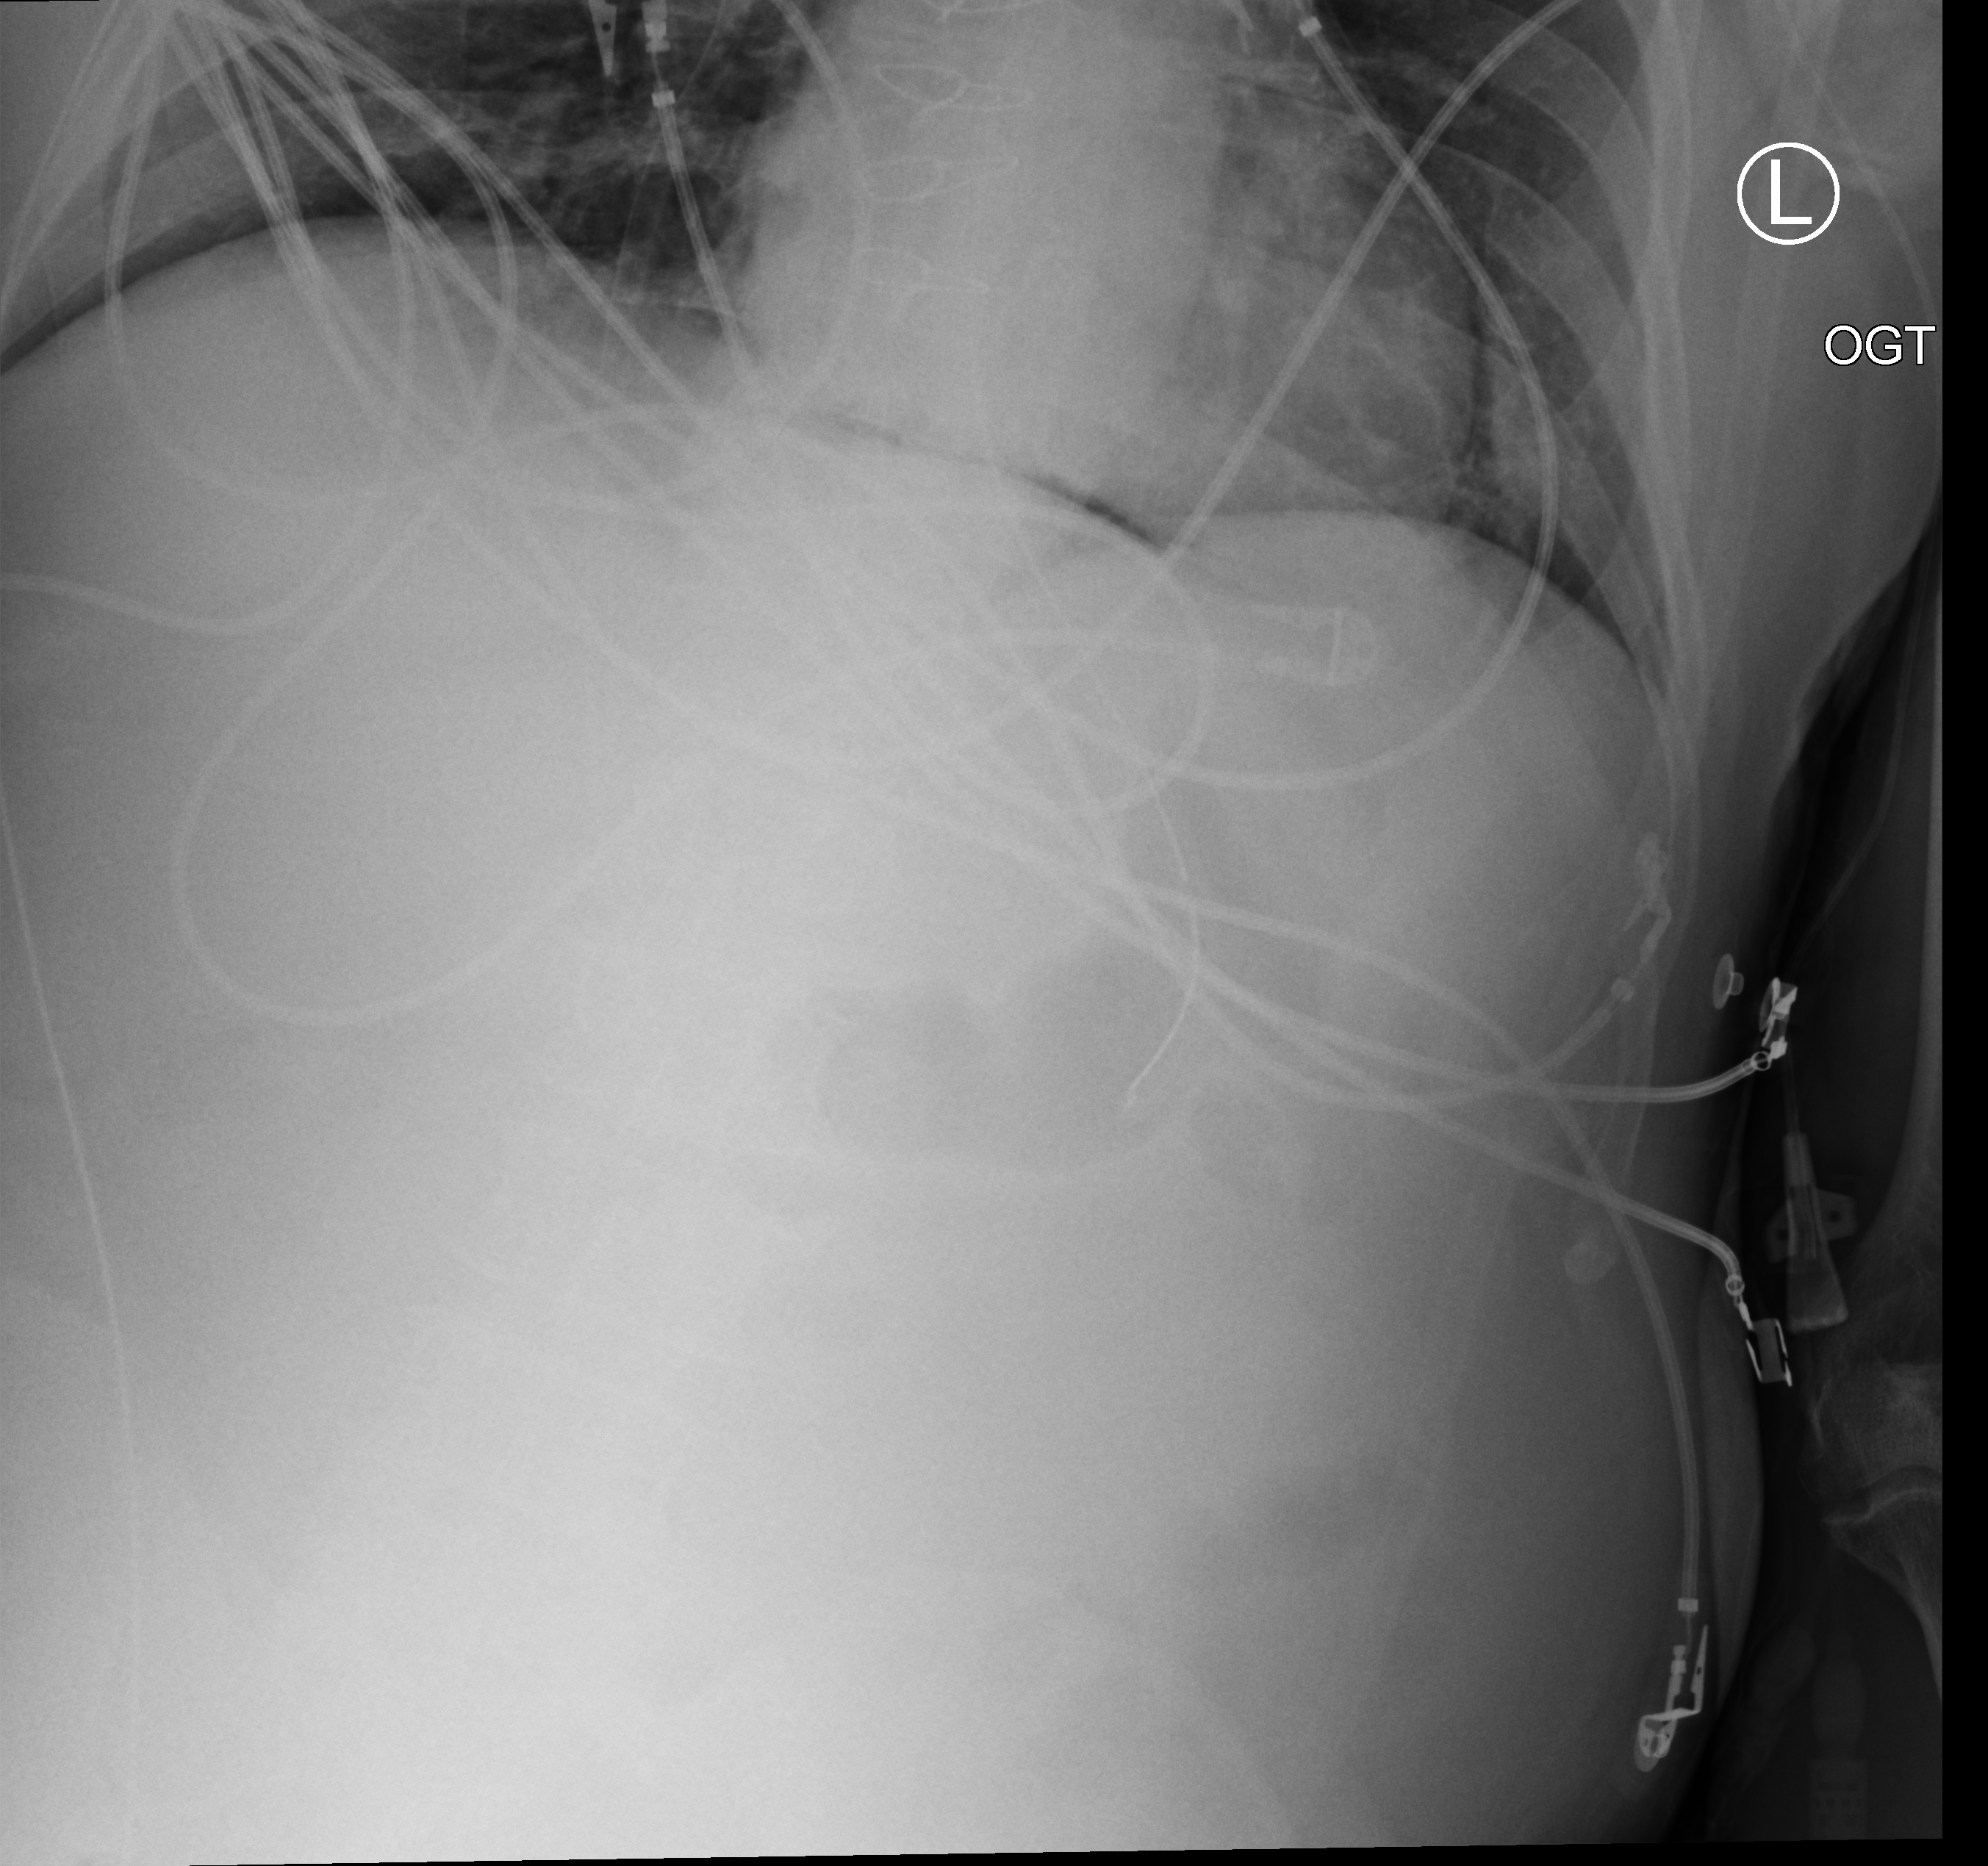
Portable chest radiograph, anteroposterior (AP) projection. Male patient hospitalised with COVID-19, age 60–74 years.
From the hospital-stay record, not from the radiograph (when in the stay this image was taken is not recorded): mechanically ventilated during this hospital stay: yes.